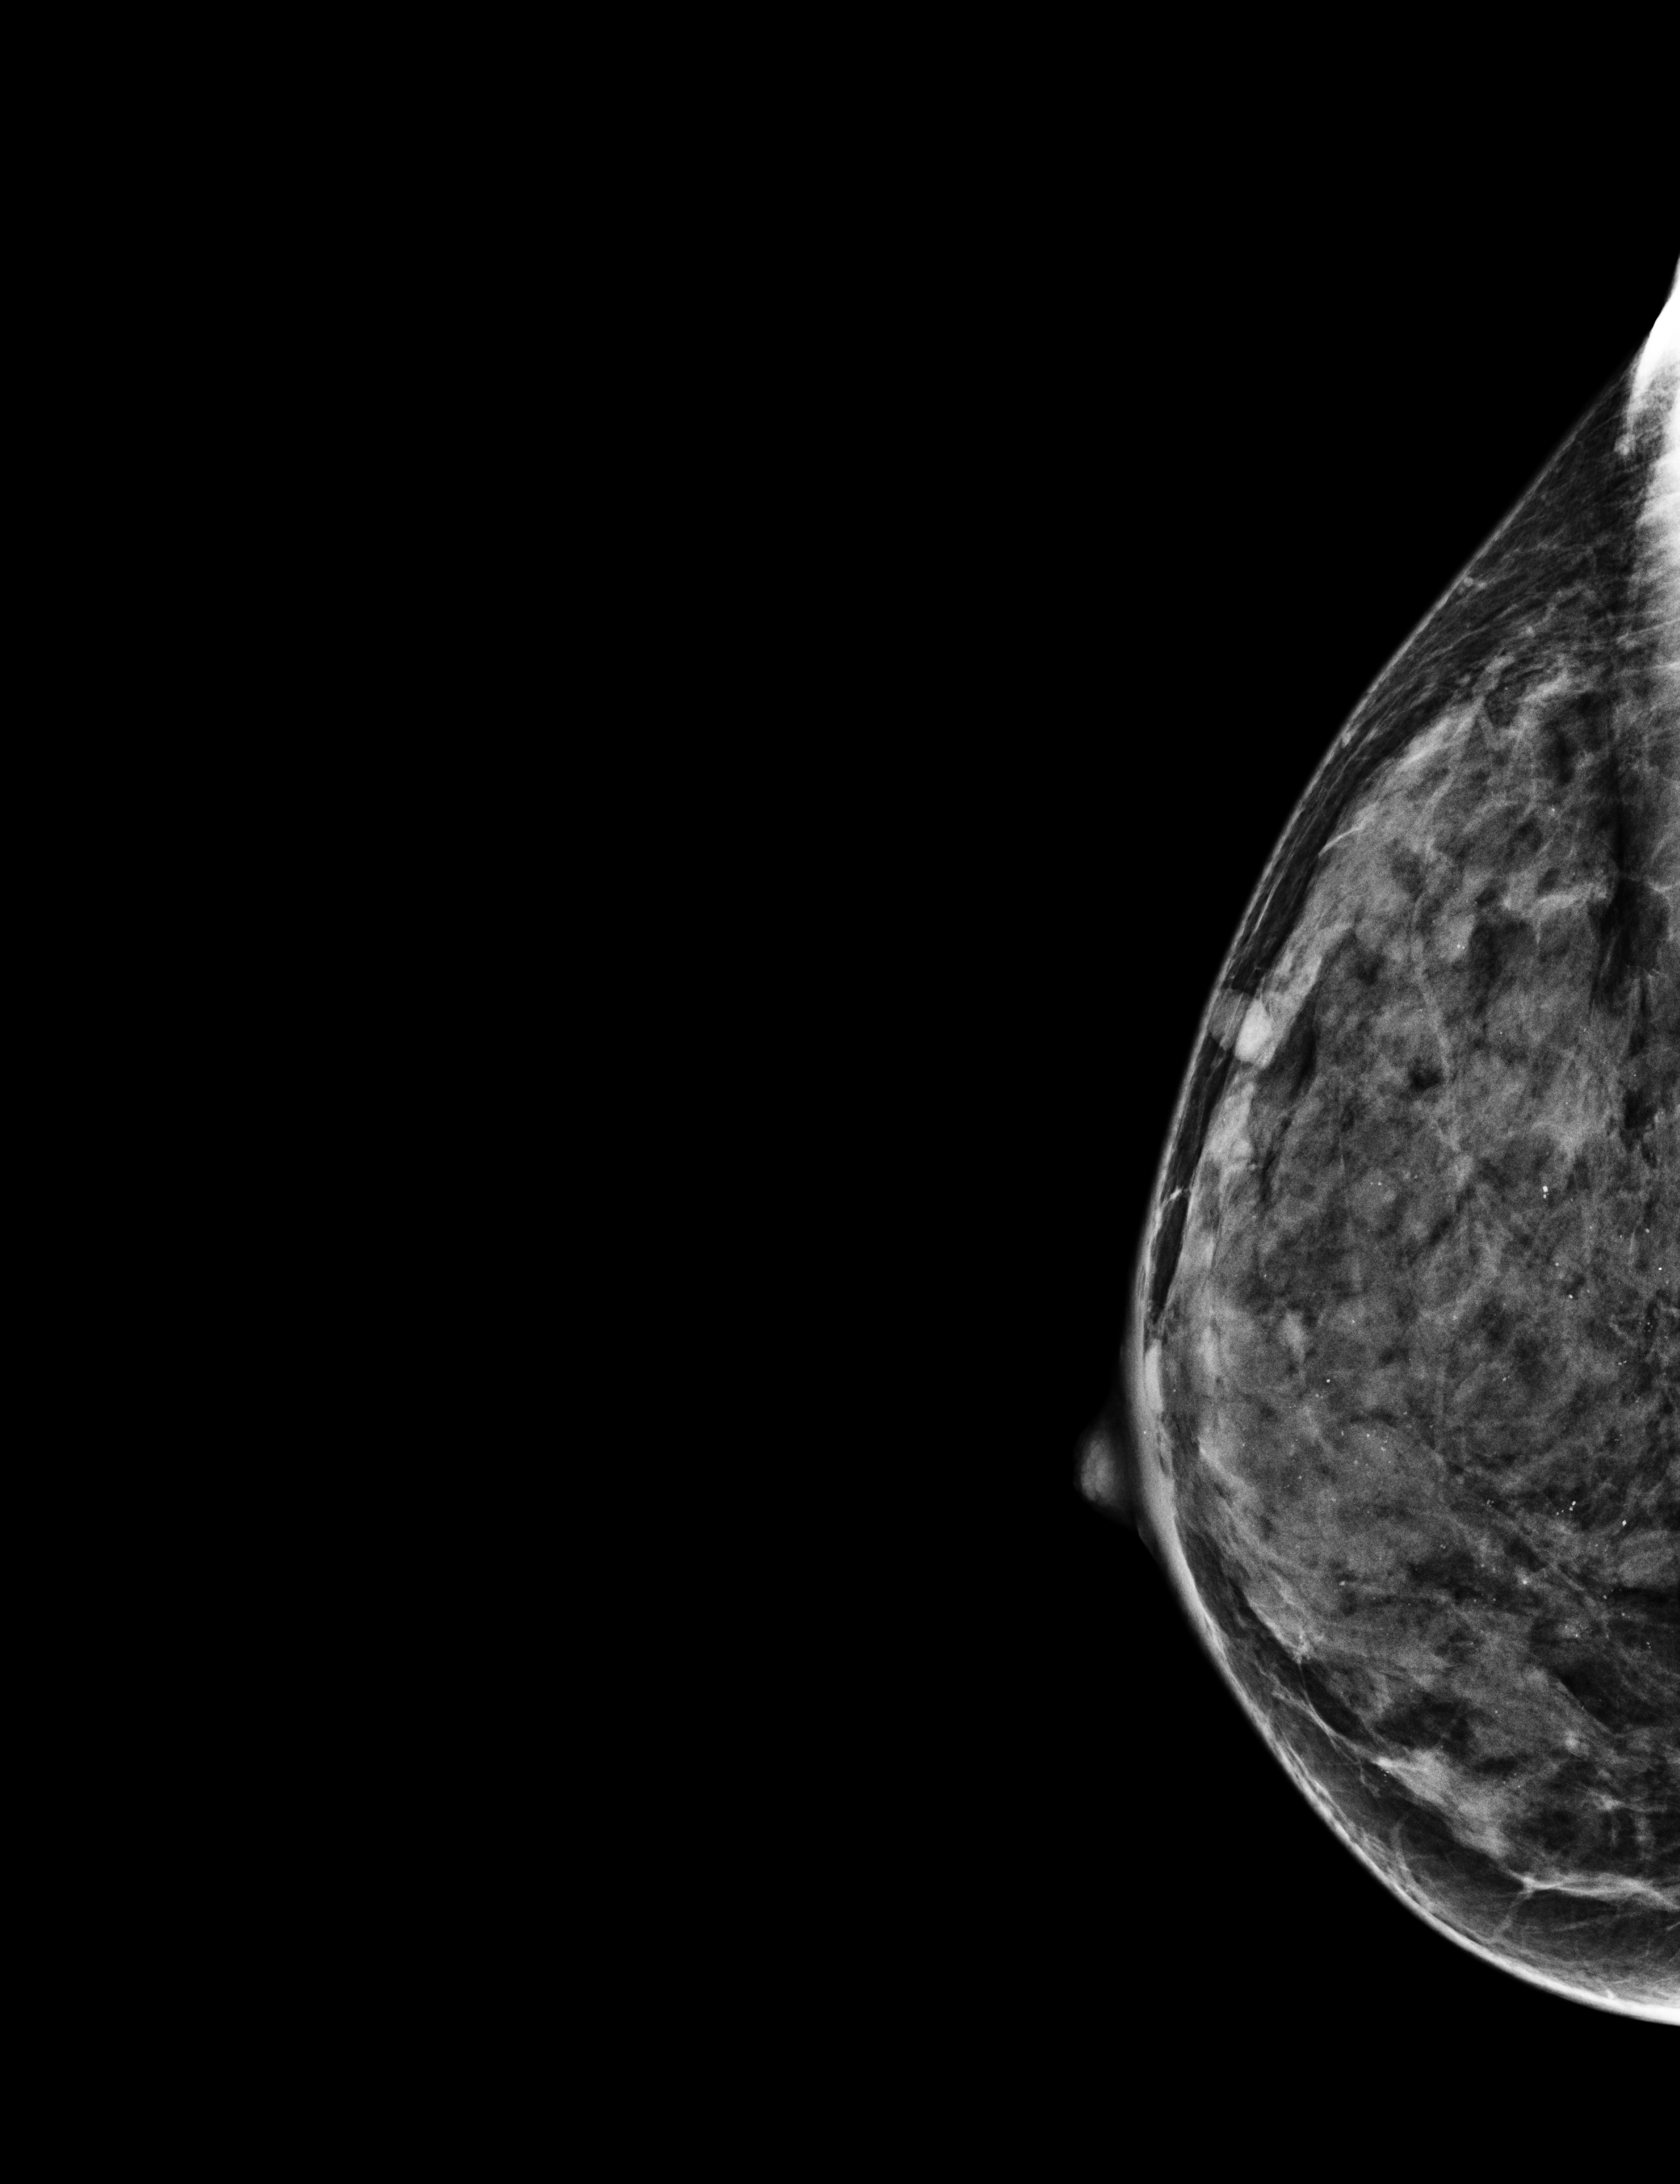
Full-field digital mammogram (FFDM), right breast, laterally exaggerated craniocaudal (XCCL) view, annual screening mammography examination, system: Selenia Dimensions. Patient: female, 49 years.
Final BI-RADS category for the screening round (tomosynthesis exam, both breasts): category 2.